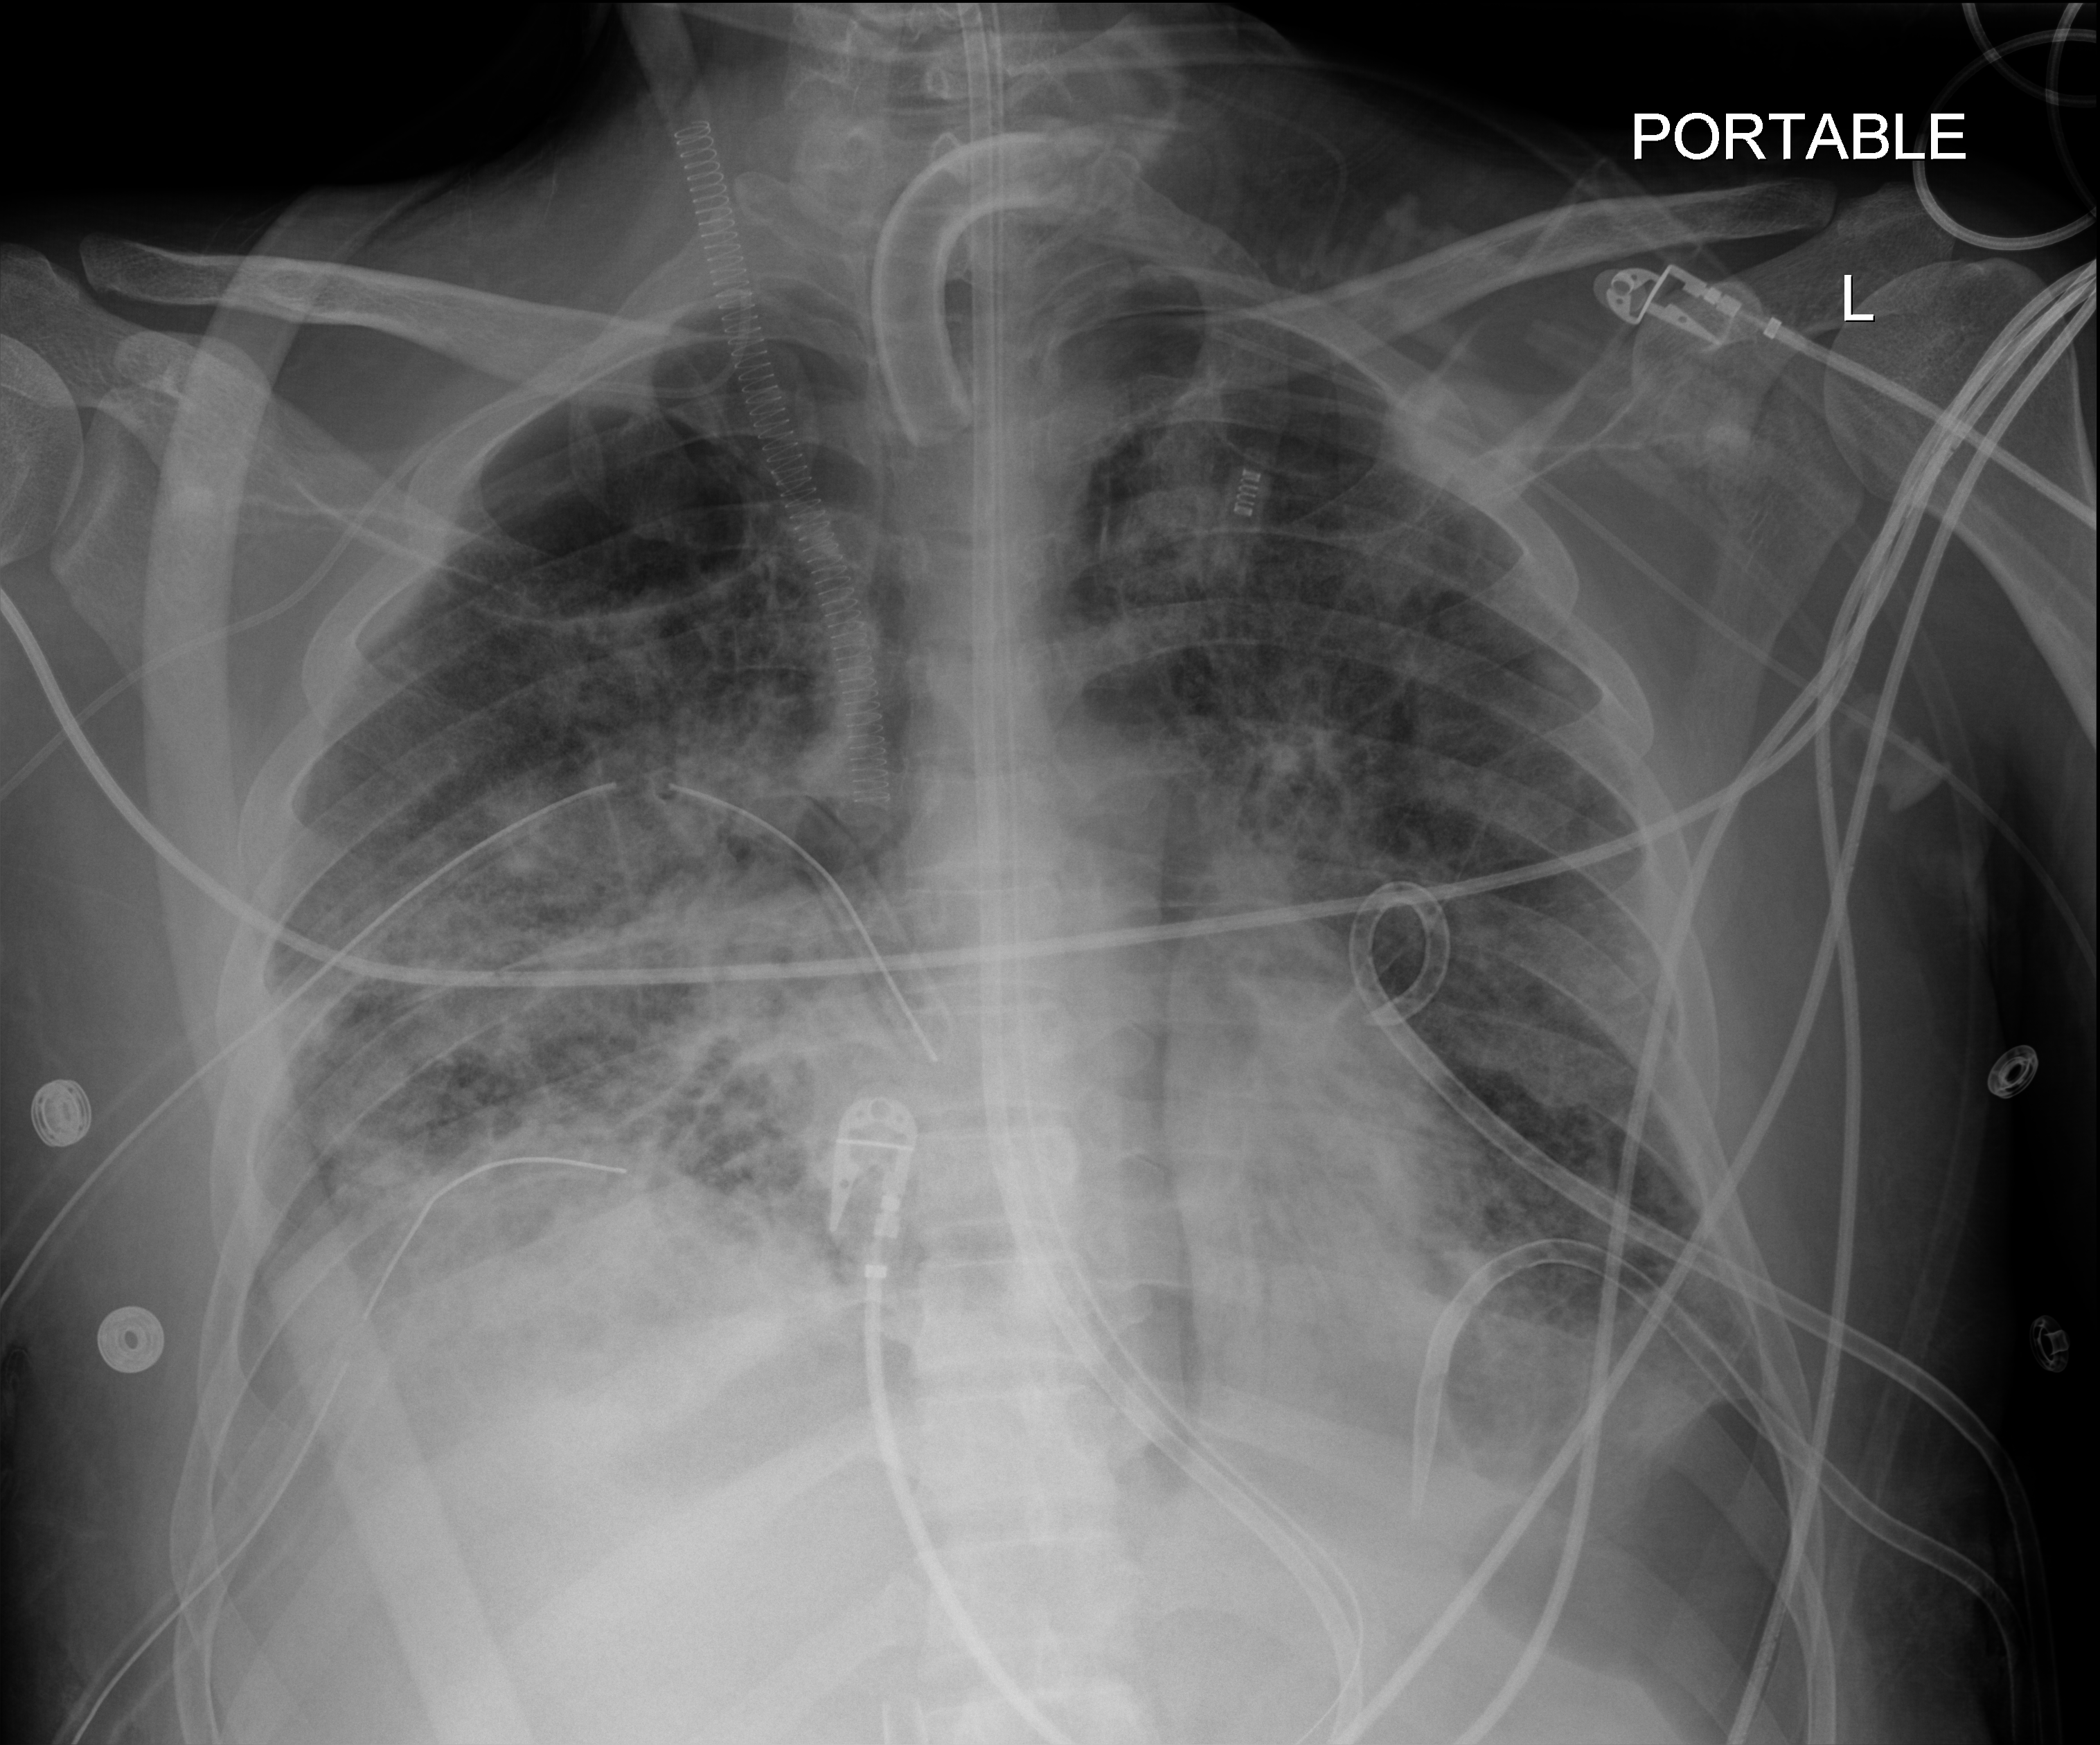
Bedside chest radiograph (digital radiography); anteroposterior (AP) projection. Patient hospitalised with COVID-19, aged 18–59 years.
From the hospital-stay record, not from the radiograph (when in the stay this image was taken is not recorded):
- length of hospital stay: 60 days
- admitted to intensive care during this hospital stay: yes